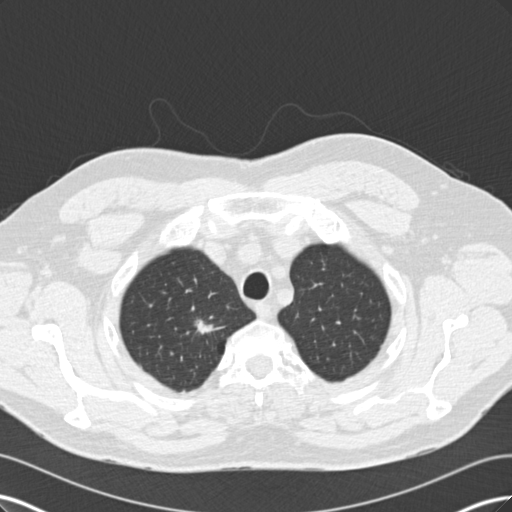
Low-dose screening chest CT, one axial slice; position 149 of 171 along the scan axis; reconstruction kernel B30f; 120 kVp; lung window (W 1500 / L -600 HU); 2 mm slice thickness; 512 × 512 image matrix.
Annotated regions visible in this slice (manually delineated by an expert):
- lesion 1 (tumor, upper lobe of right lung): box from (x=195, y=319) to (x=213, y=334) px